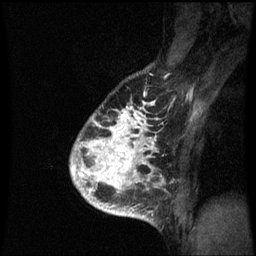
Breast MRI (dynamic contrast-enhanced), one sagittal slice. Slice 50 of 60 in the series (ordered by position). Dynamic contrast-enhanced series, image 2 of 3 at this slice position (ordered by acquisition). 1.5 T. TE 4.2 ms, TR 8.9 ms. 2 mm slice thickness. 256 × 256 image matrix, field of view 200 × 200 mm. Female patient, age 35 years. Case-level facts recorded for this patient, not image findings: setting: breast cancer imaged before/during neoadjuvant chemotherapy; receptor status: HR-positive, HER2-negative.
Structures marked on this image (semi-automatic segmentation, software-assisted and operator-edited):
- analysis volume of interest (the breast-tissue region the enhancement analysis was run in; not a lesion): bounding box [x1, y1, x2, y2] px = [72, 100, 164, 215]
- tumour enhancement mask (voxels above the 70 % enhancement threshold inside the analysis volume of interest): [72, 102, 156, 215]